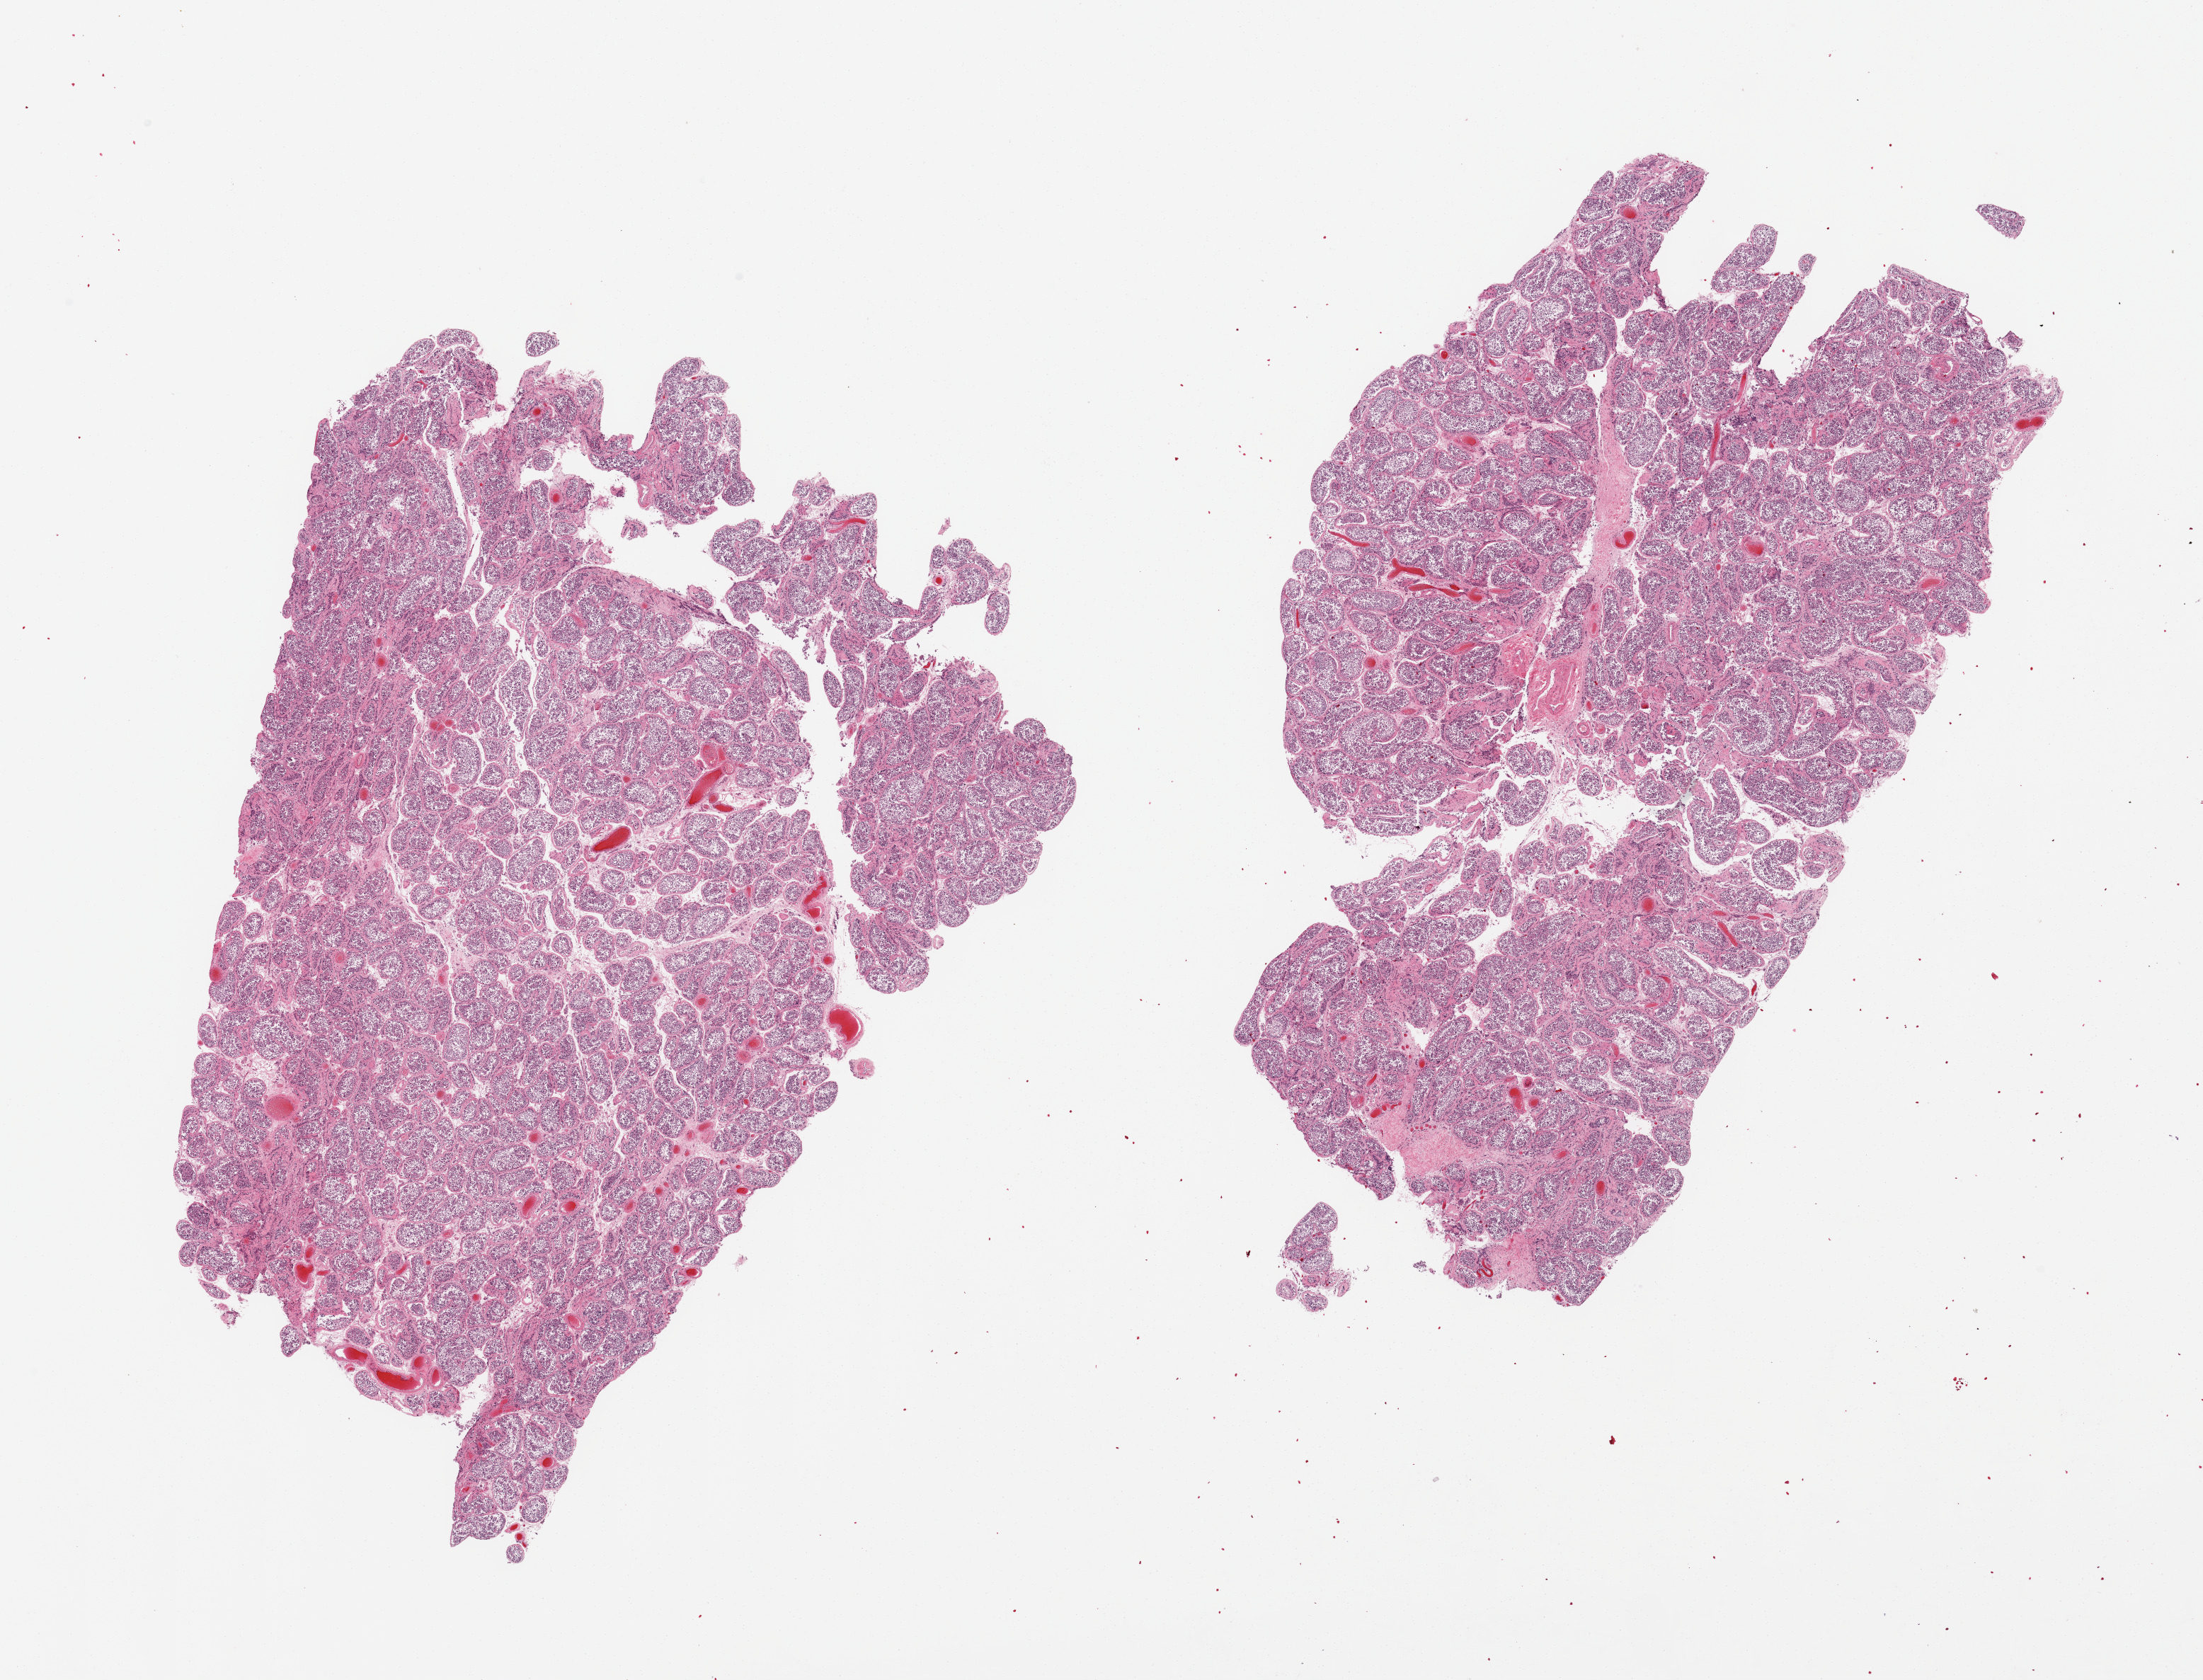
Haematoxylin and eosin whole-slide image, brightfield — whole scanned area (about 24.6 x 18.8 mm, acquisition: 20x scan) shown as a low-resolution overview, PAXgene-fixed paraffin-embedded (PFPE) section, target tissue: testis, donor tissue sample. Donor sex: male.
* reviewer comment on this tissue sample: 2 pieces; active spermatogenesis